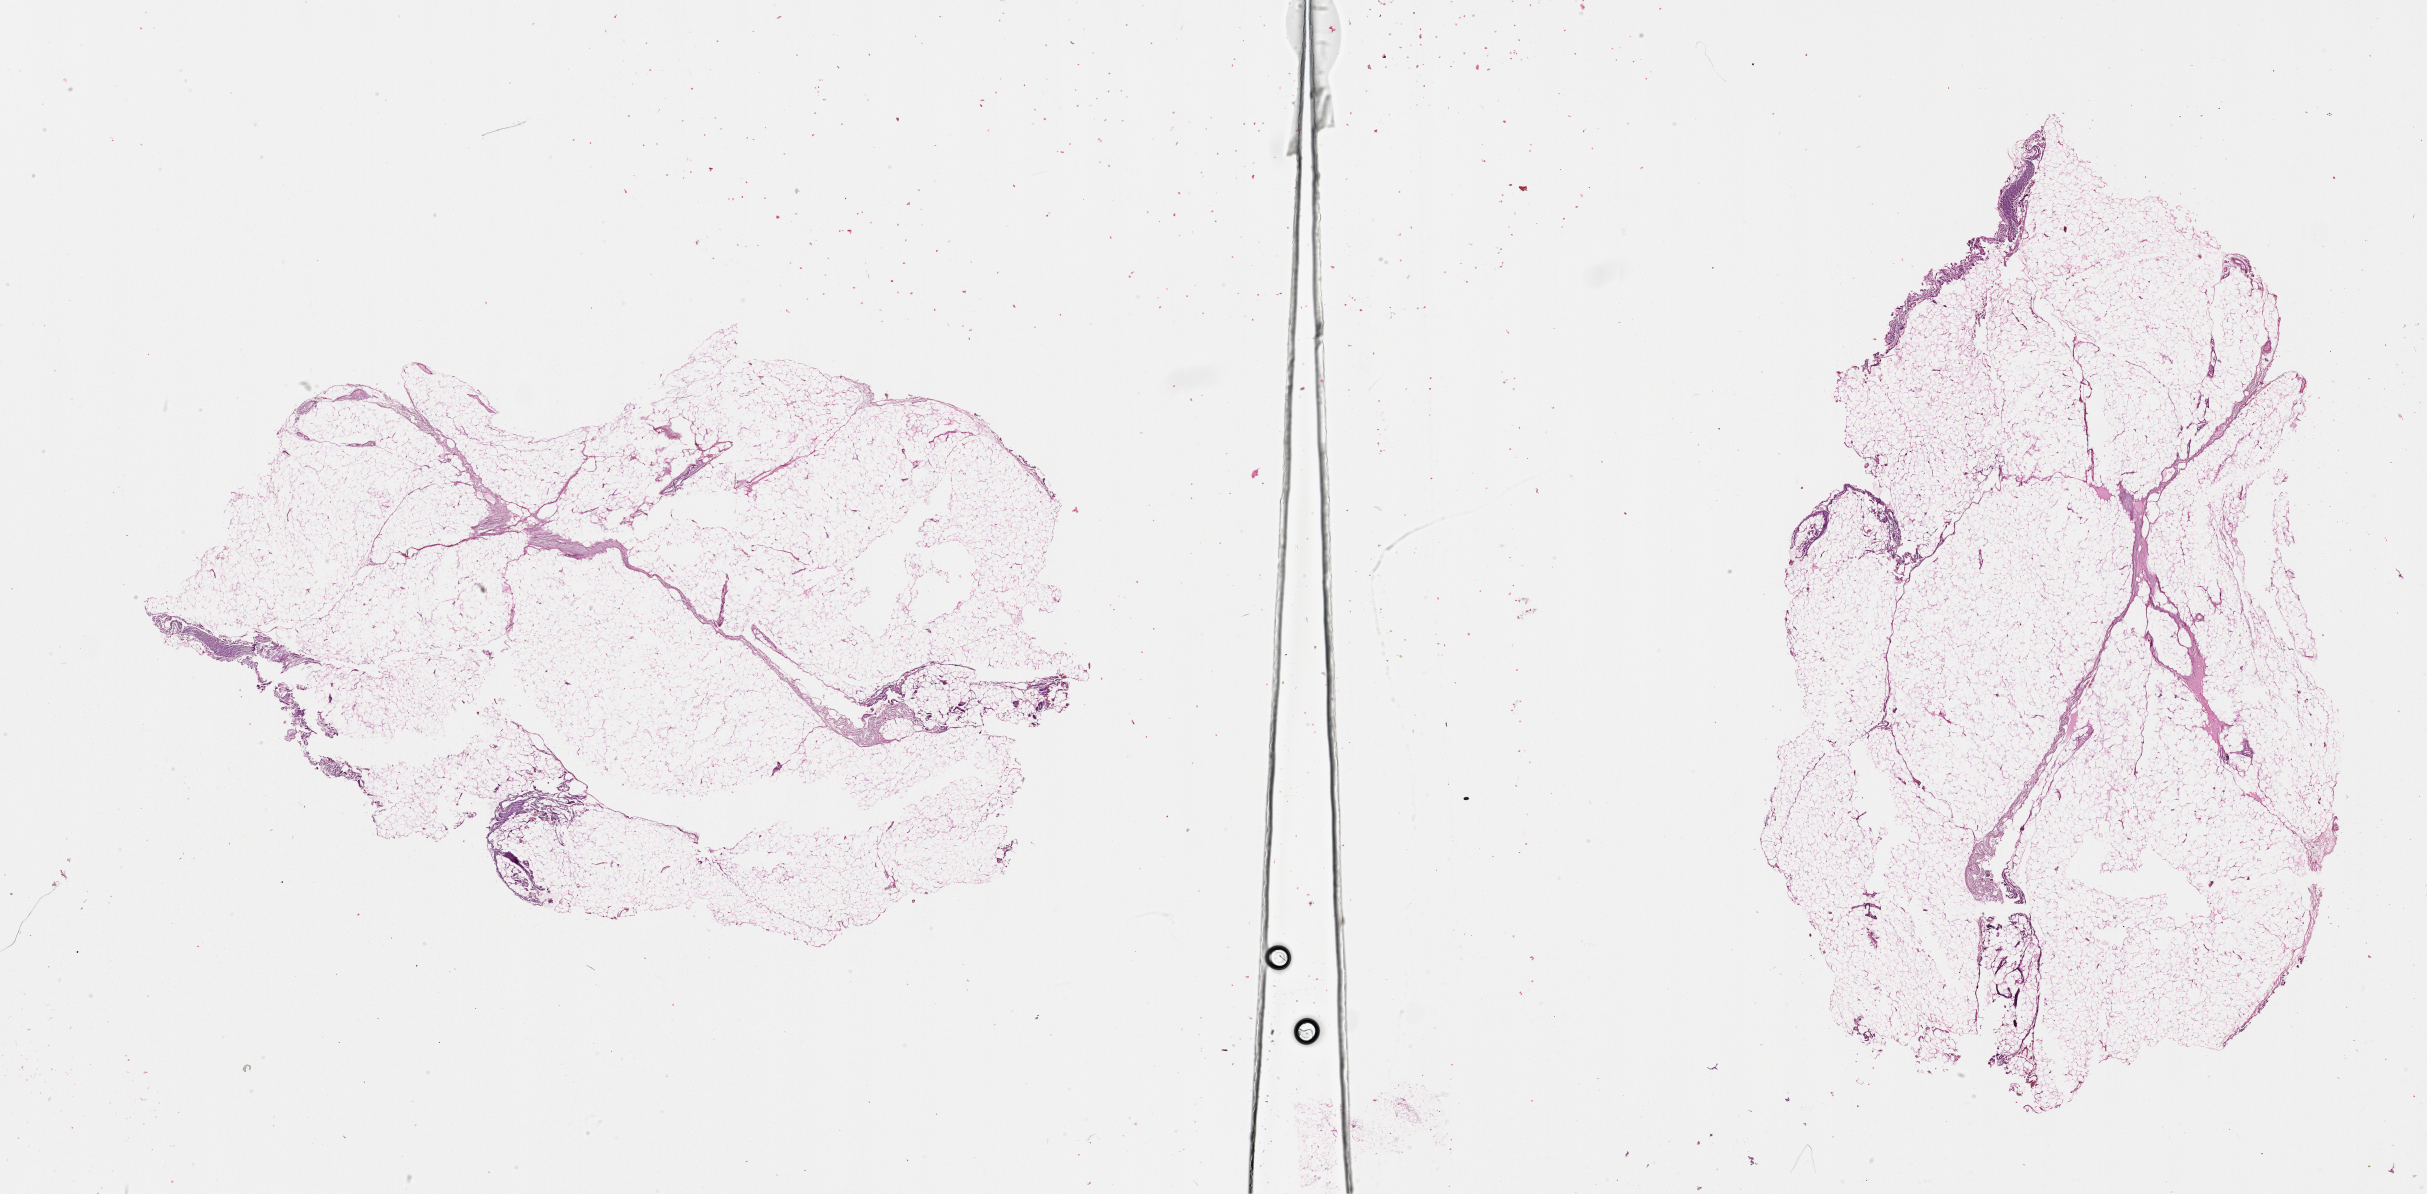
Whole-slide histology image, H&E-stained — low-resolution overview of the scanned area, about 39.1 x 19.2 mm (acquisition: 20x scan), normal (non-tumour) tissue sample, sampled site: skin. Female, 80 y/o.
This section: normal (non-tumour) tissue from the same patient. Patient diagnosis: Malignant melanoma, NOS.